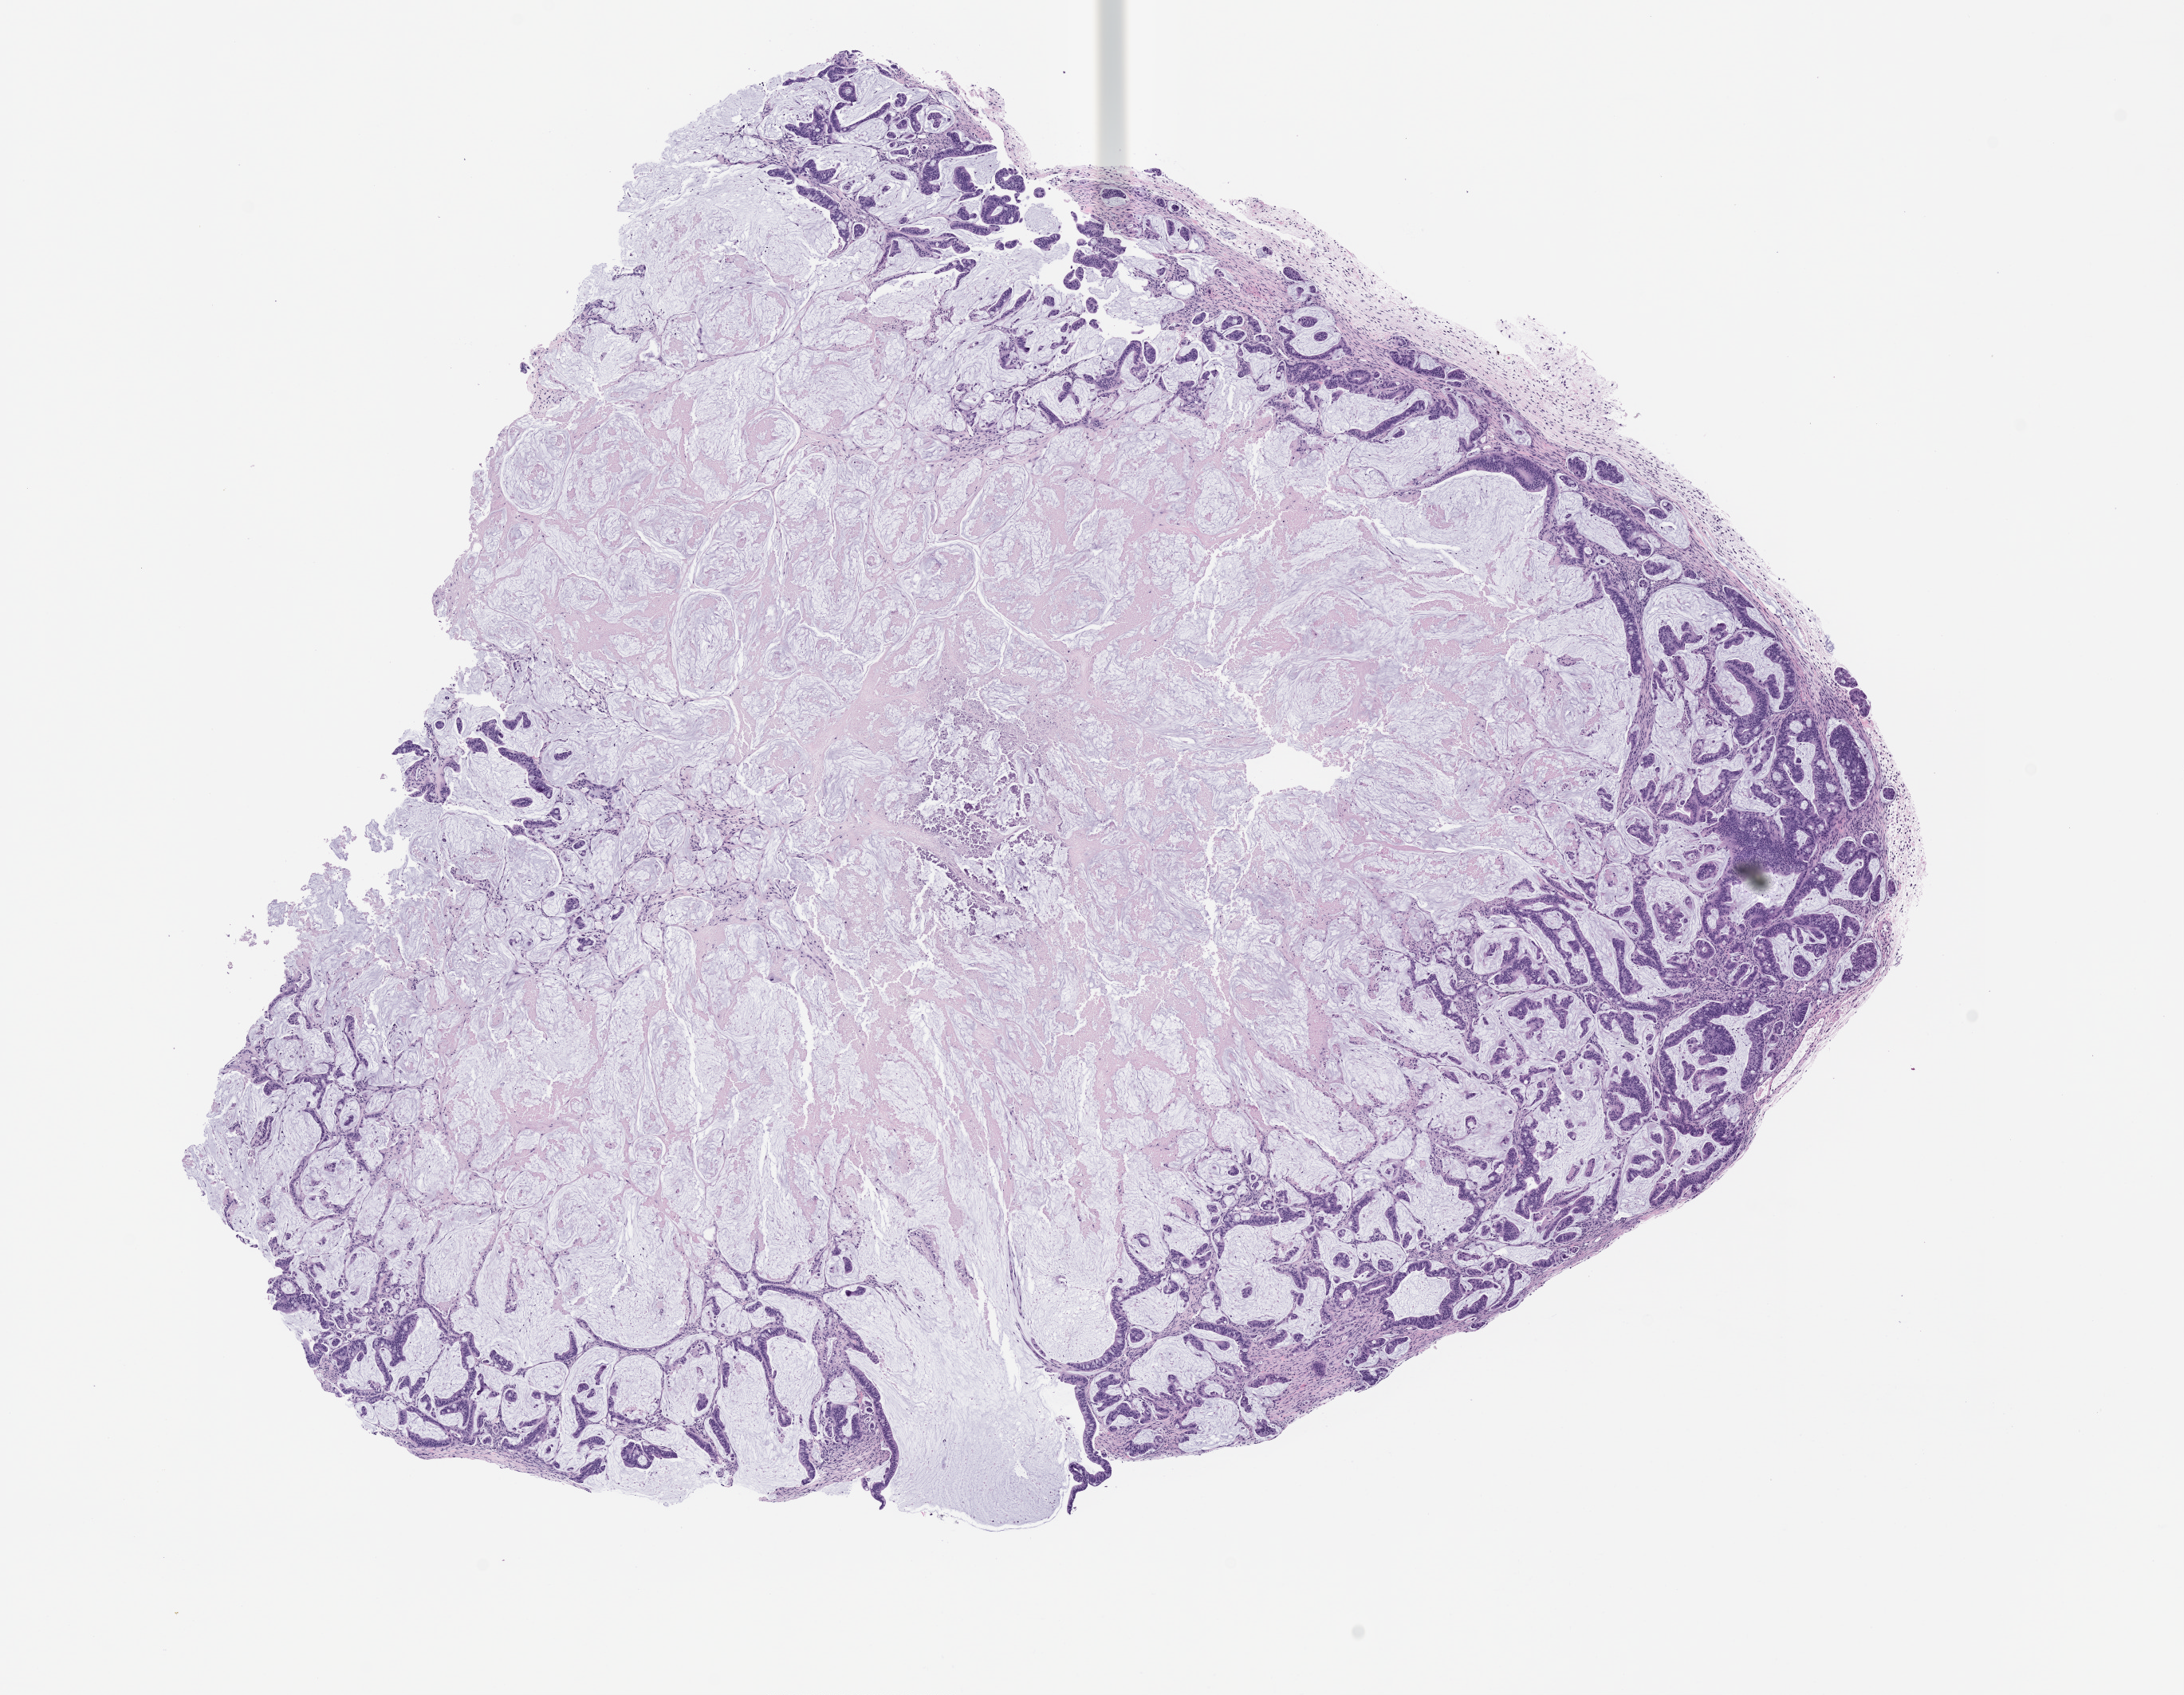
H&E whole-slide image of a patient-derived xenograft (PDX) tumor grown in a mouse, passage 3, a low-resolution overview of the entire scanned area, about 11.0 x 8.5 mm. Formalin-fixed paraffin-embedded section. Originating tumor site category: rectum.
Originating patient diagnosis: Rectal Adenocarcinoma.